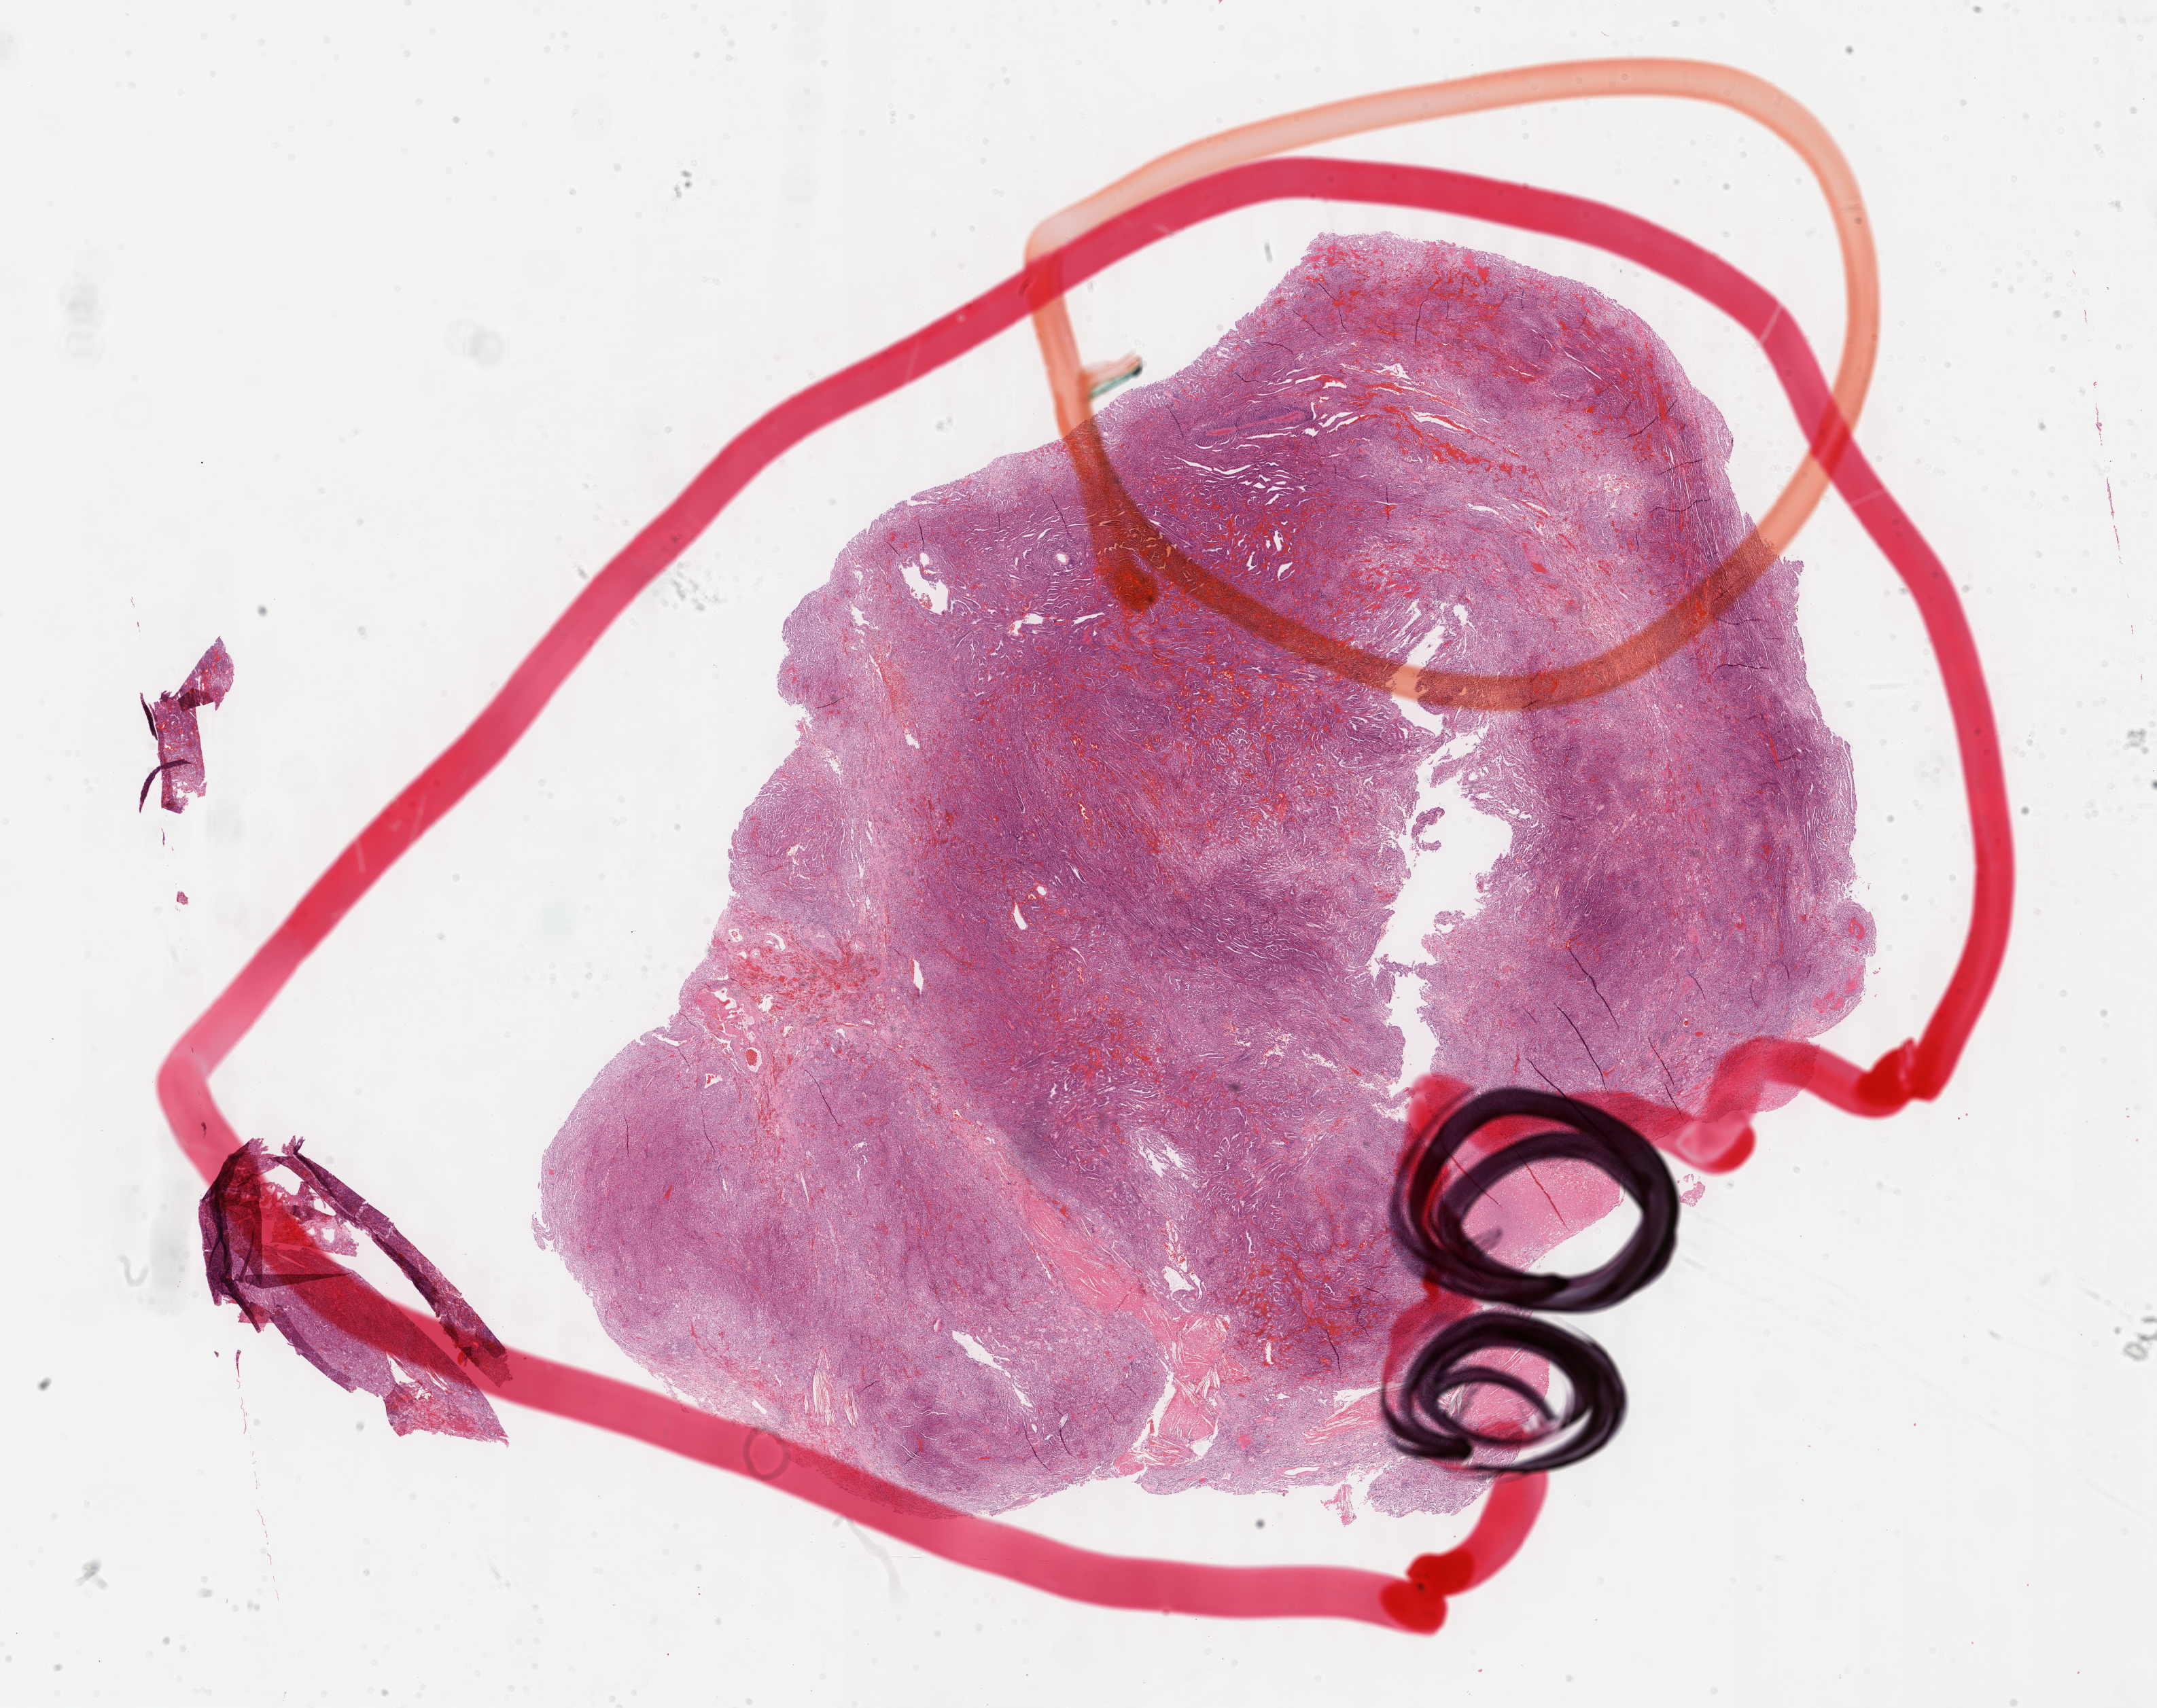
Hematoxylin and eosin (H&E) stained whole-slide image, shown as a low-resolution overview of the whole scanned area (about 25.7 x 20.3 mm); FFPE section; kidney, primary tumour sample. Female patient; age at initial diagnosis 75 years.
TNM: T1a NX M0. AJCC pathologic stage: I (7th edition). Pathologic diagnosis: Papillary adenocarcinoma, NOS.